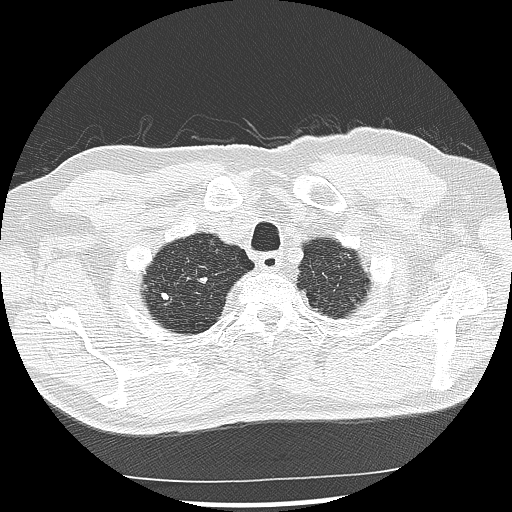
Low-dose screening chest CT, one axial slice. Position 124 of 142 along the scan axis. Lung window (W 1500 / L -600 HU). 512 × 512 image matrix.
Annotated regions visible in this slice (expert manual segmentation):
- lesion 3 (nodule, upper lobe of right lung): box from (x=195, y=277) to (x=208, y=293) px